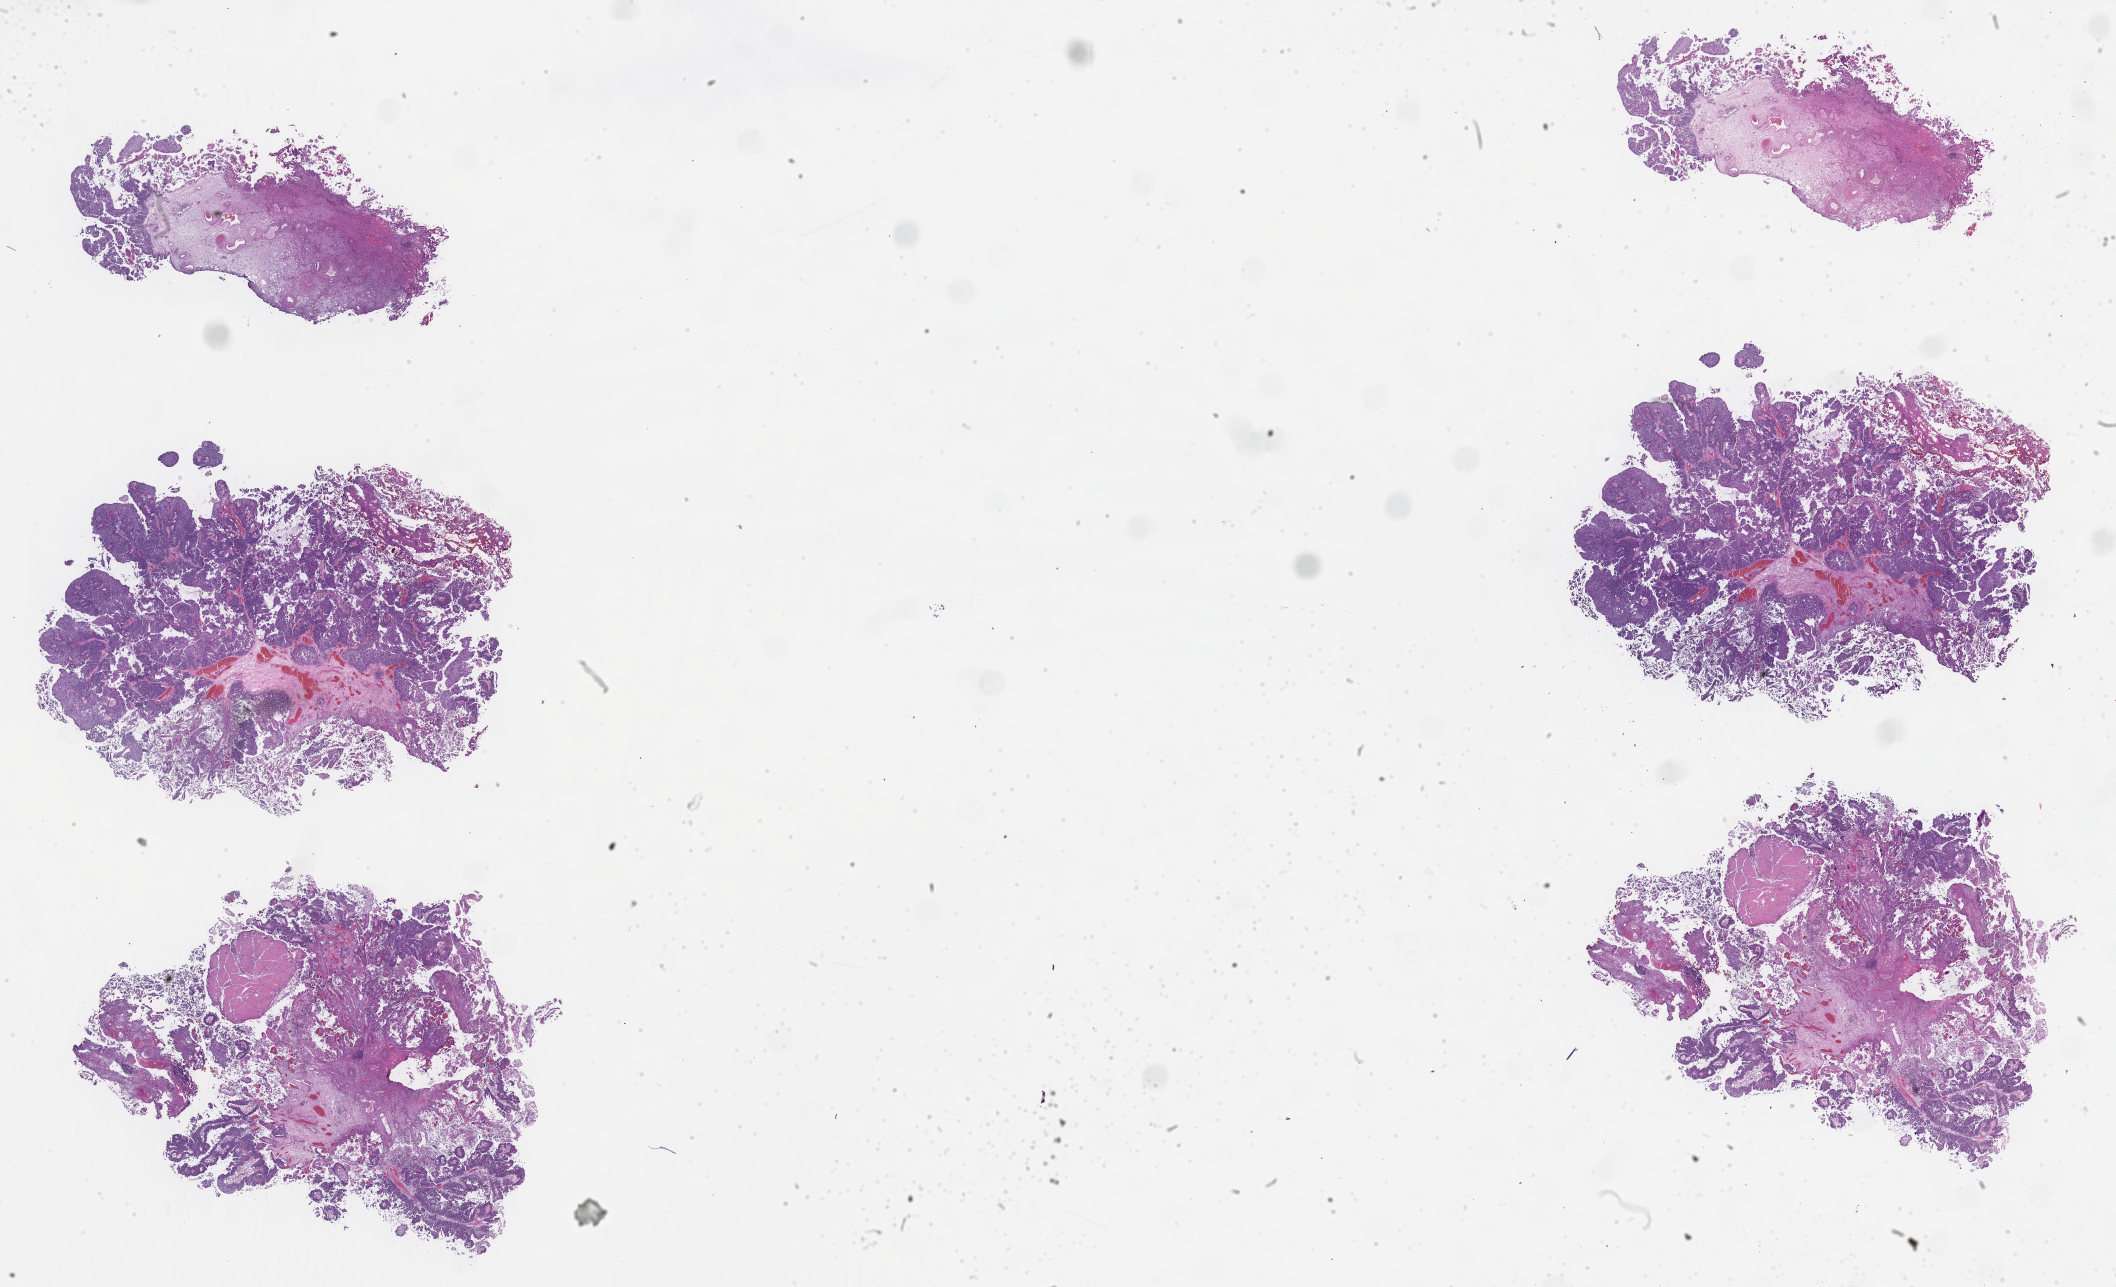
Hematoxylin and eosin (H&E) whole-slide image — whole scanned area (about 34.1 x 20.8 mm) shown as a low-resolution overview, FFPE section, primary tumor, anatomic site: bladder. Male, age 62 years at initial diagnosis. Pathologist review of this section (percent, as recorded): tumor cells 70%, tumor nuclei 90%, stromal cells 30%, necrosis 0%, normal cells 0%. Infiltration values recorded for this section: lymphocyte infiltration 0%, monocyte infiltration 0%, neutrophil infiltration 0%.
- histologic diagnosis: Papillary urothelial carcinoma, non-invasive